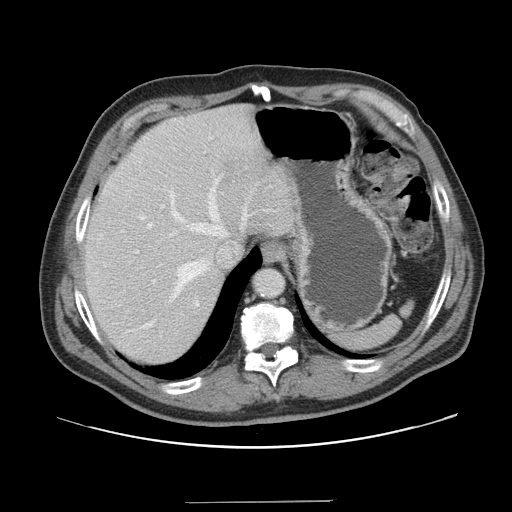
Contrast-enhanced abdominal CT, one axial slice. Position 124 of 151 along the scan axis. Intravenous contrast given. Soft-tissue window (W 400 / L 40 HU). 2.5 mm slice thickness. 512 × 512 image matrix. Male patient, age 63 years. From the clinical record (not read from this slice): diagnosis: colorectal cancer liver metastases, imaged before liver resection; multiple liver metastases: no; largest metastasis: 2.1 cm; disease in both lobes: no.
Structures marked on this image (outlined manually by an expert reader):
- hepatic veins: bounding box (x1, y1, x2, y2) in pixels: (140, 180, 248, 326)
- liver: (84, 106, 296, 365)
- planned liver remnant (the part of the liver to remain after resection): (84, 118, 254, 365)
- portal vein (with intrahepatic branches): (135, 205, 165, 283)
- liver metastasis: (221, 163, 236, 185)